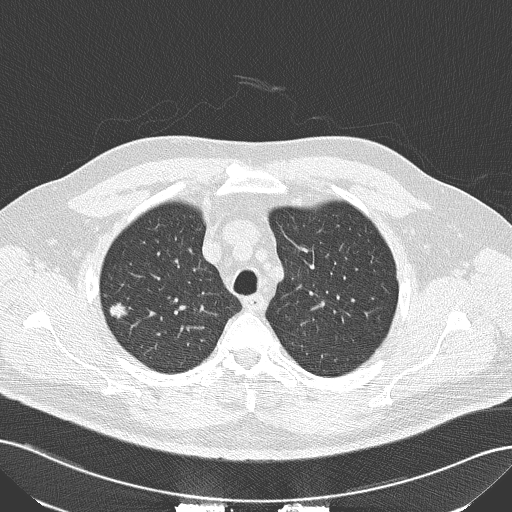
Low-dose screening chest CT, one axial slice; position 119 of 152 along the scan axis; 120 kVp; lung window (W 1500 / L -600 HU); 512 × 512 image matrix, field of view 360 × 360 mm.
Outlined on this slice (expert manual segmentation):
- lesion 1 (tumor, upper lobe of right lung): bounding box [x1, y1, x2, y2] px = [110, 303, 128, 319]